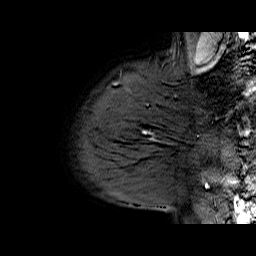
Breast MRI (dynamic contrast-enhanced), one sagittal slice; position 56 of 70 along the scan axis; dynamic contrast-enhanced series, time point 2 of 6 at this slice position (early post-contrast); 1.5 T; TE 6.5 ms, TR 33 ms; 4 mm slice thickness; 256 × 256 image matrix, field of view 200 × 200 mm. Female patient. Case-level facts recorded for this patient, not image findings: setting: breast cancer imaged before/during neoadjuvant chemotherapy; receptor status: HER2-positive.
Outlined on this slice (semi-automatically segmented with operator editing):
- analysis volume of interest (the breast-tissue region the enhancement analysis was run in; not a lesion): bounding box [x1, y1, x2, y2] px = [113, 112, 174, 170]
- tumour enhancement mask (voxels above the 100 % enhancement threshold inside the analysis volume of interest): [142, 130, 147, 134]